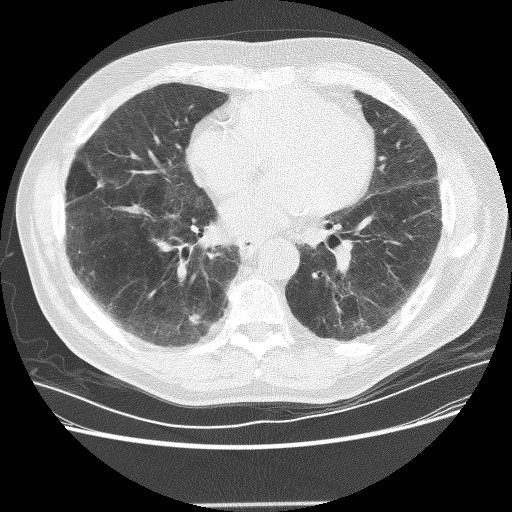
Low-dose screening chest CT, axial slice, baseline screening round, lung window (W 1500 / L -600 HU), 2.5 mm slice thickness, lung (sharp) reconstruction kernel (BONE), slice 149 of 281 in the series, 512 × 512 image matrix. Male participant, aged 72 years at enrolment. Former smoker at enrolment.
Lesion marked by an expert reader, box from (x=170, y=307) to (x=210, y=343) px. The screening reader recorded 2 non-calcified nodules or masses ≥4 mm on this exam (right lower lobe, left lower lobe); which of them this box marks is not recorded. Official screen result: positive, change unspecified: nodule(s) >= 4 mm or enlarging nodule(s), mass(es), or other non-specific abnormalities suspicious for lung cancer. Lung cancer was diagnosed 436 days after this screen: squamous cell carcinoma, NOS, right lower lobe, poorly differentiated (G3), stage IB (AJCC 6th edition), 42 mm at pathology.